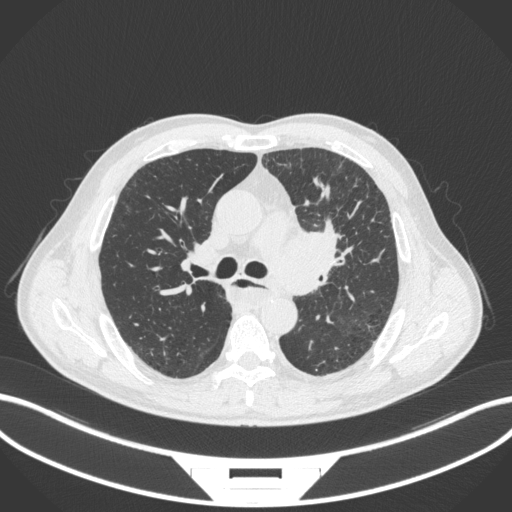
Chest CT, one axial slice; position 242 of 411 along the scan axis; 120 kVp; lung window (W 1500 / L -600 HU); 1 mm slice thickness; 512 × 512 image matrix, field of view 400 × 400 mm. Male patient, age 57 years. From the clinical record (not read from this slice): clinical TNM (as recorded): T2a N1 M0.
Structures marked on this image (bounding box drawn by a radiologist):
- lung tumour (recorded histology: squamous cell carcinoma): bounding box (x1, y1, x2, y2) in pixels: (267, 219, 344, 296)